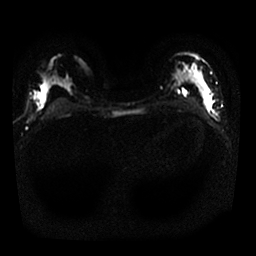
Breast MRI, one axial slice. Diffusion-weighted series; image 2 of 4 stored at this slice position (different b-values; order by instance number). 1.5 T. 256 × 256 image matrix. Female patient.
Outlined on this slice (manually delineated by an expert):
- tumour on diffusion-weighted imaging: box from (x=196, y=71) to (x=212, y=106) px